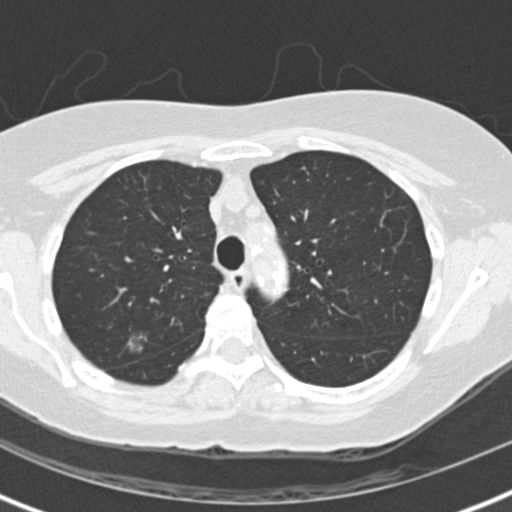
Low-dose screening chest CT, one axial slice; slice 104 of 147 in the series (ordered by position); reconstruction kernel B30f; 120 kVp; lung window (W 1500 / L -600 HU); 2 mm slice thickness; 512 × 512 image matrix.
Structures marked on this image (manually delineated by an expert):
- lesion 1 (tumor, upper lobe of right lung): bounding box (x1, y1, x2, y2) in pixels: (130, 336, 147, 352)